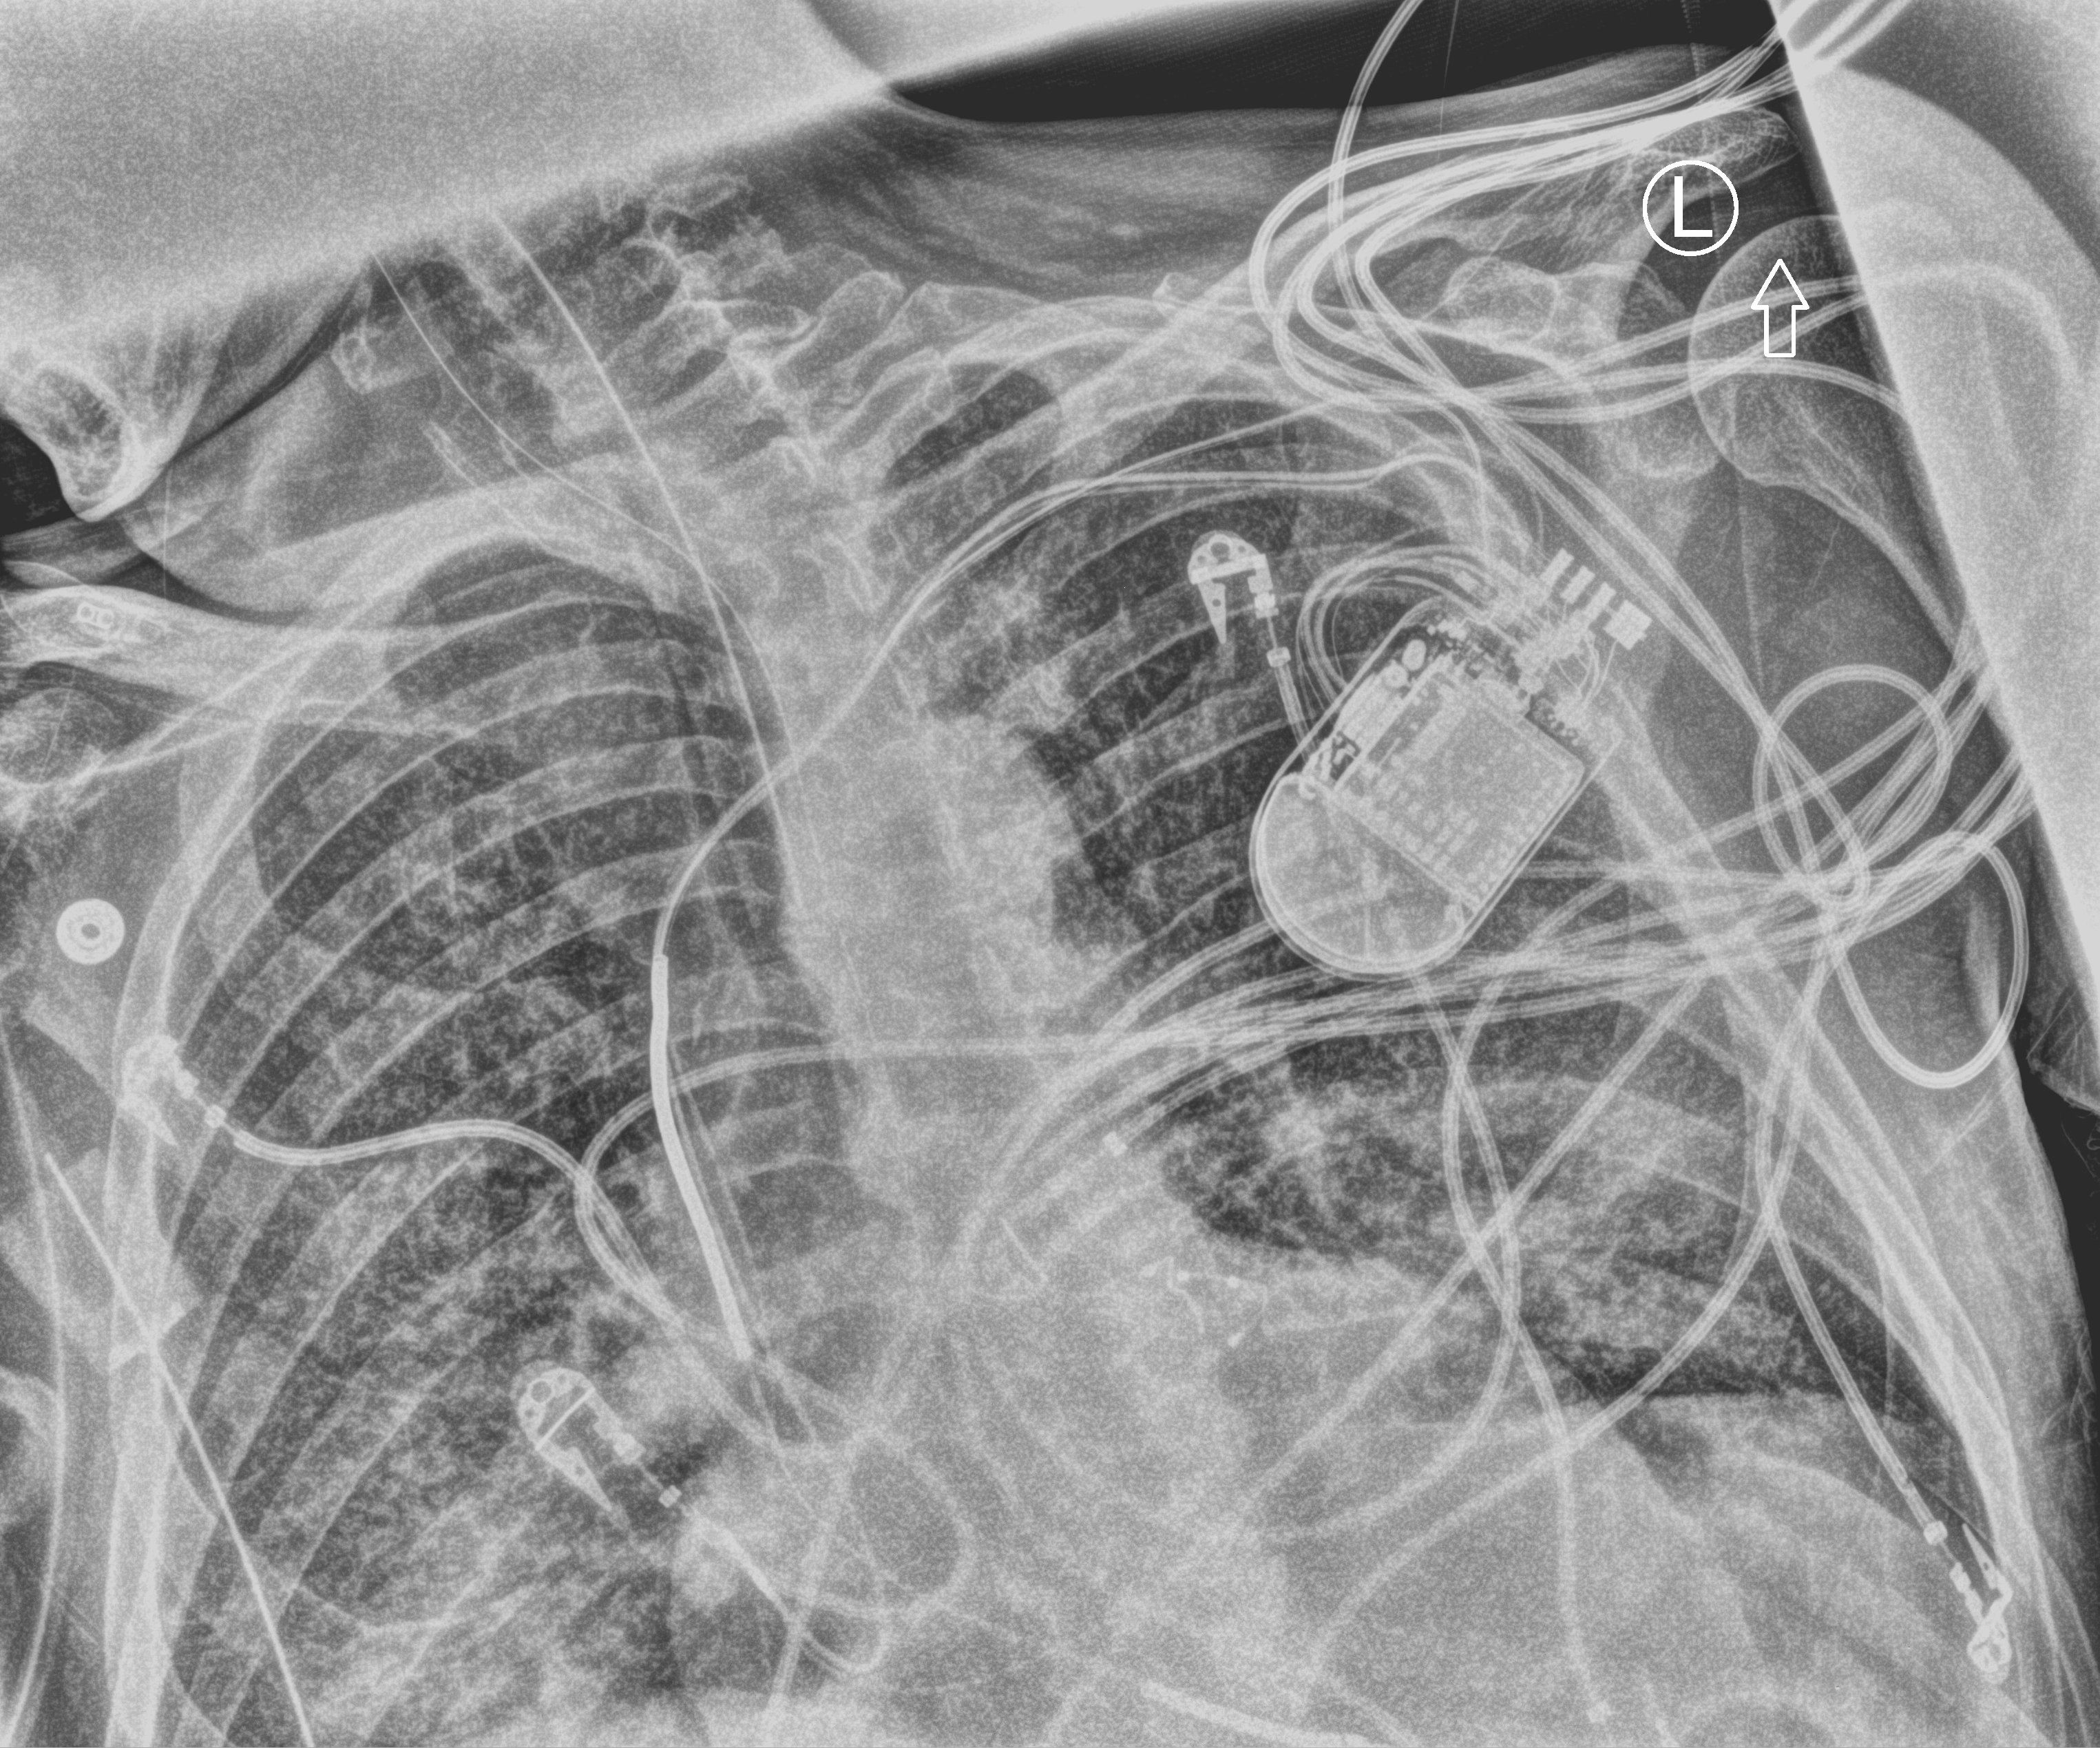
Chest X-ray (portable), anteroposterior (AP) projection. Patient hospitalised with COVID-19; male, aged 60–74 years.
Hospital-stay facts (about this admission, not read from this image; timing relative to this image not recorded):
- mechanically ventilated during this hospital stay: yes